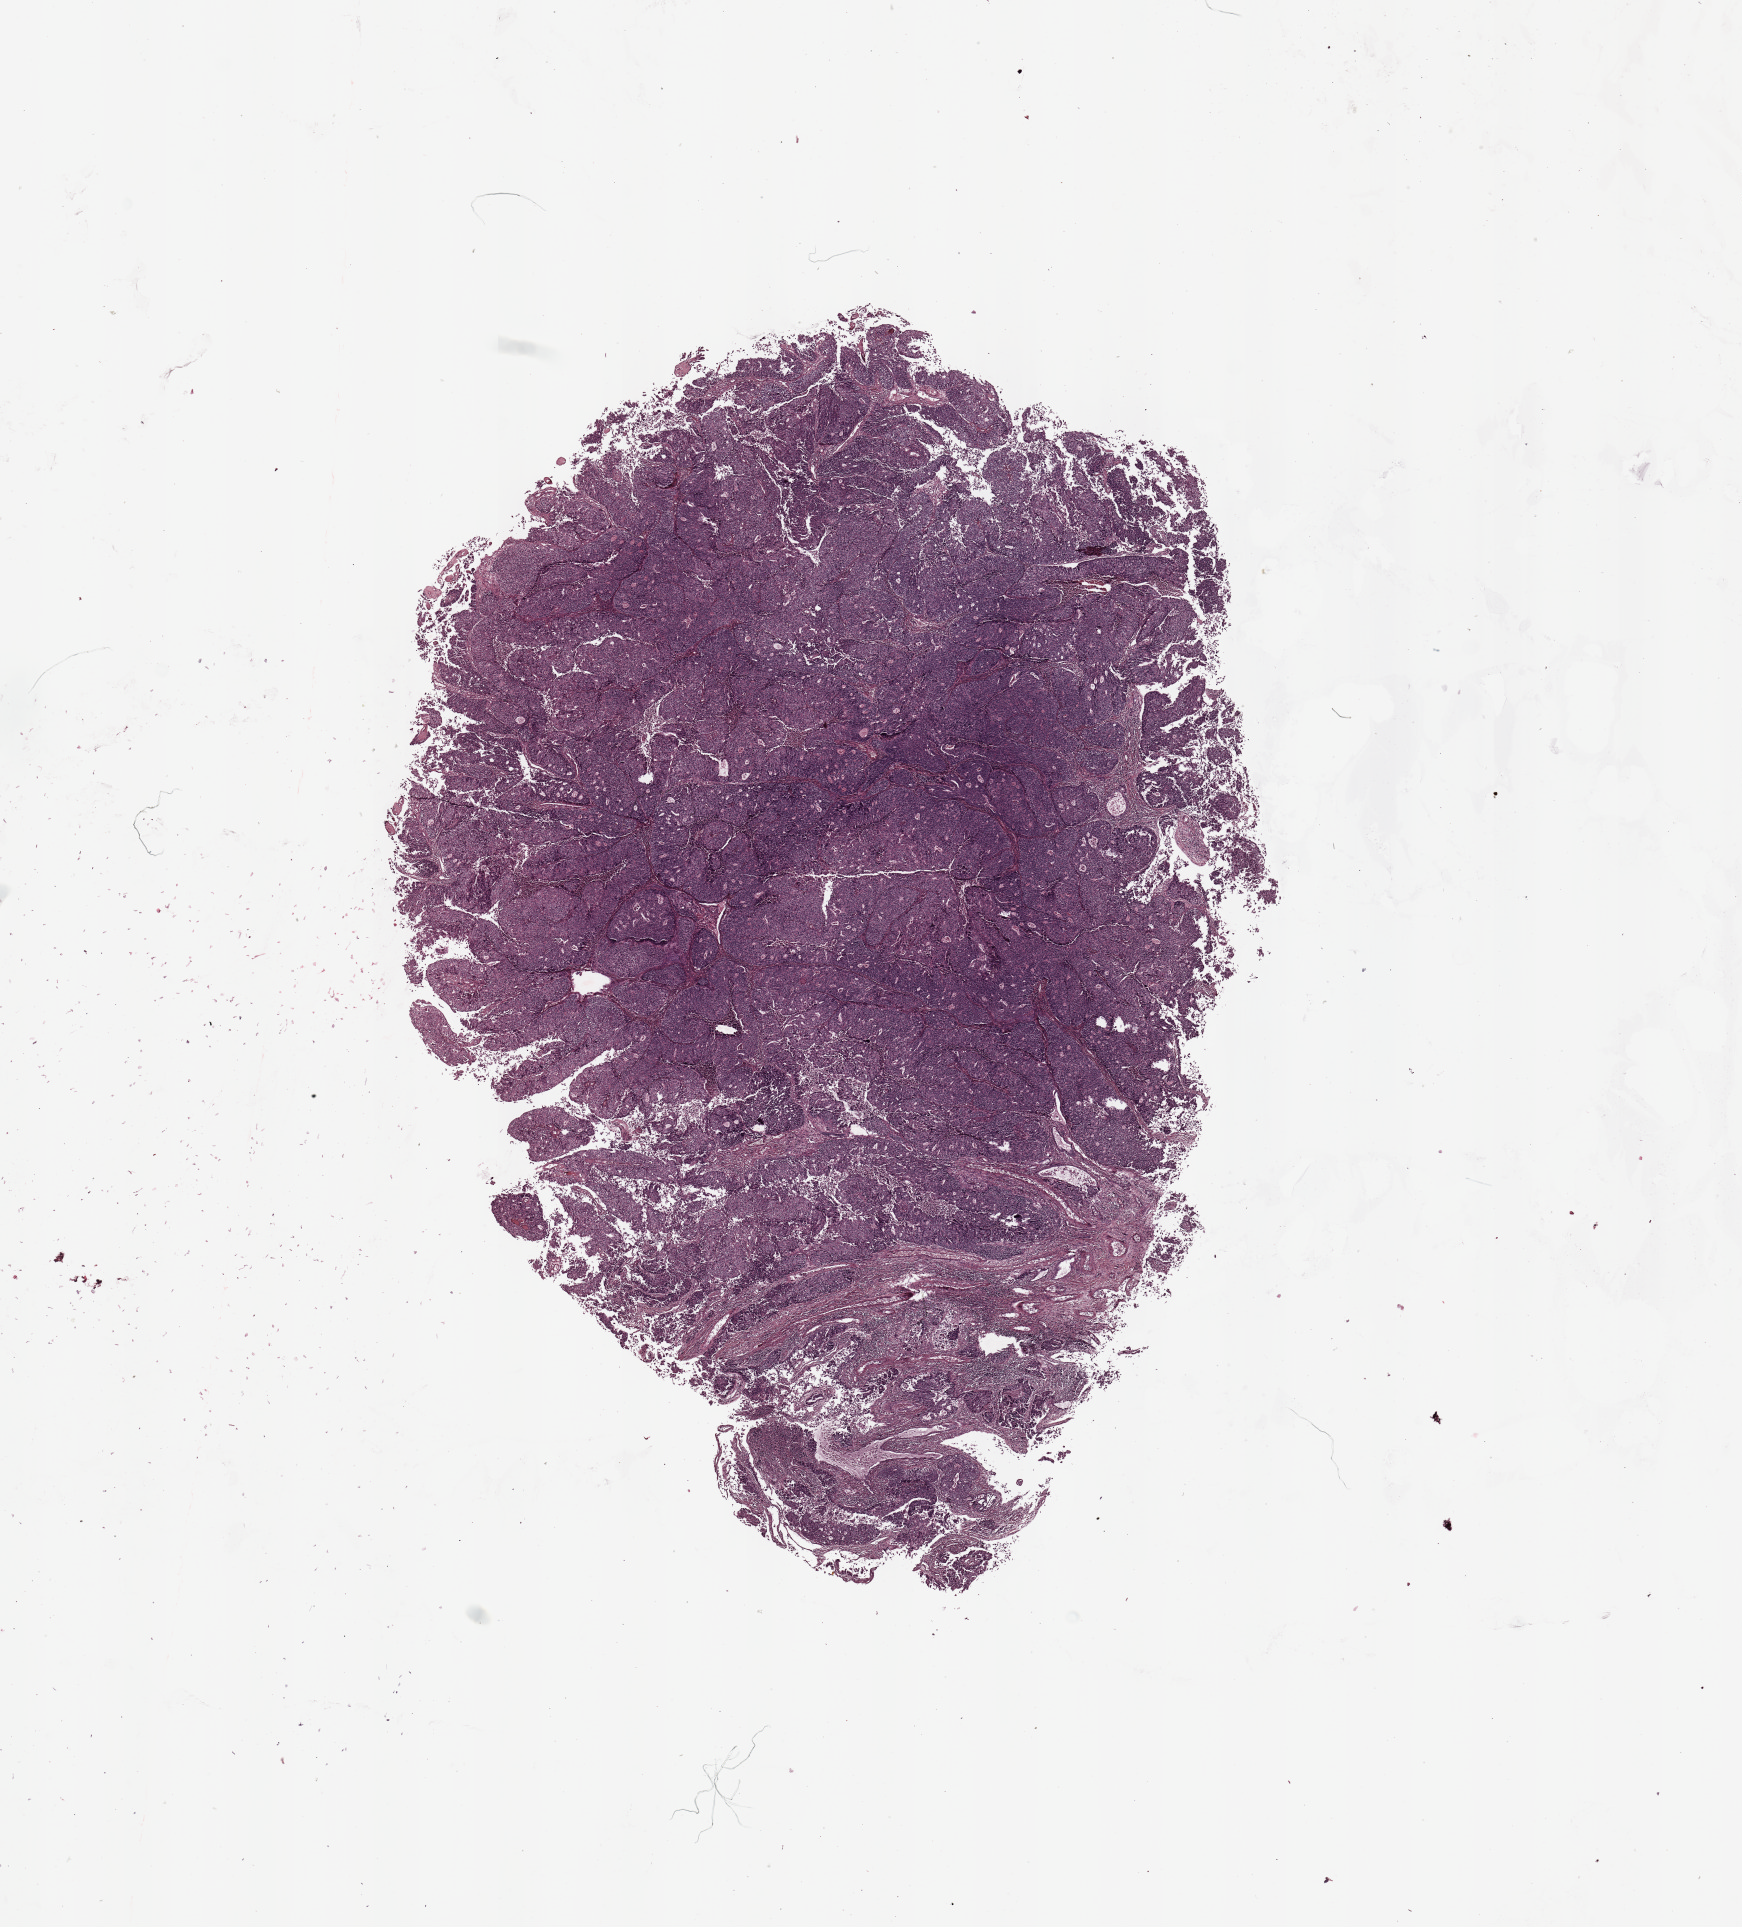
Digitized H&E-stained tissue section (whole slide), a low-resolution overview of the entire scanned area, about 13.8 x 15.2 mm (acquisition: 20x scan), tumour tissue sample, sampled site: uterus. Patient: female, age 75 years. Histologic grade: G3 (poorly differentiated). Pathologist review of this section (percent, as recorded): tumour nuclei 90%, necrosis 5%.
• AJCC pathologic stage: I
• diagnosis: Endometrioid adenocarcinoma, NOS